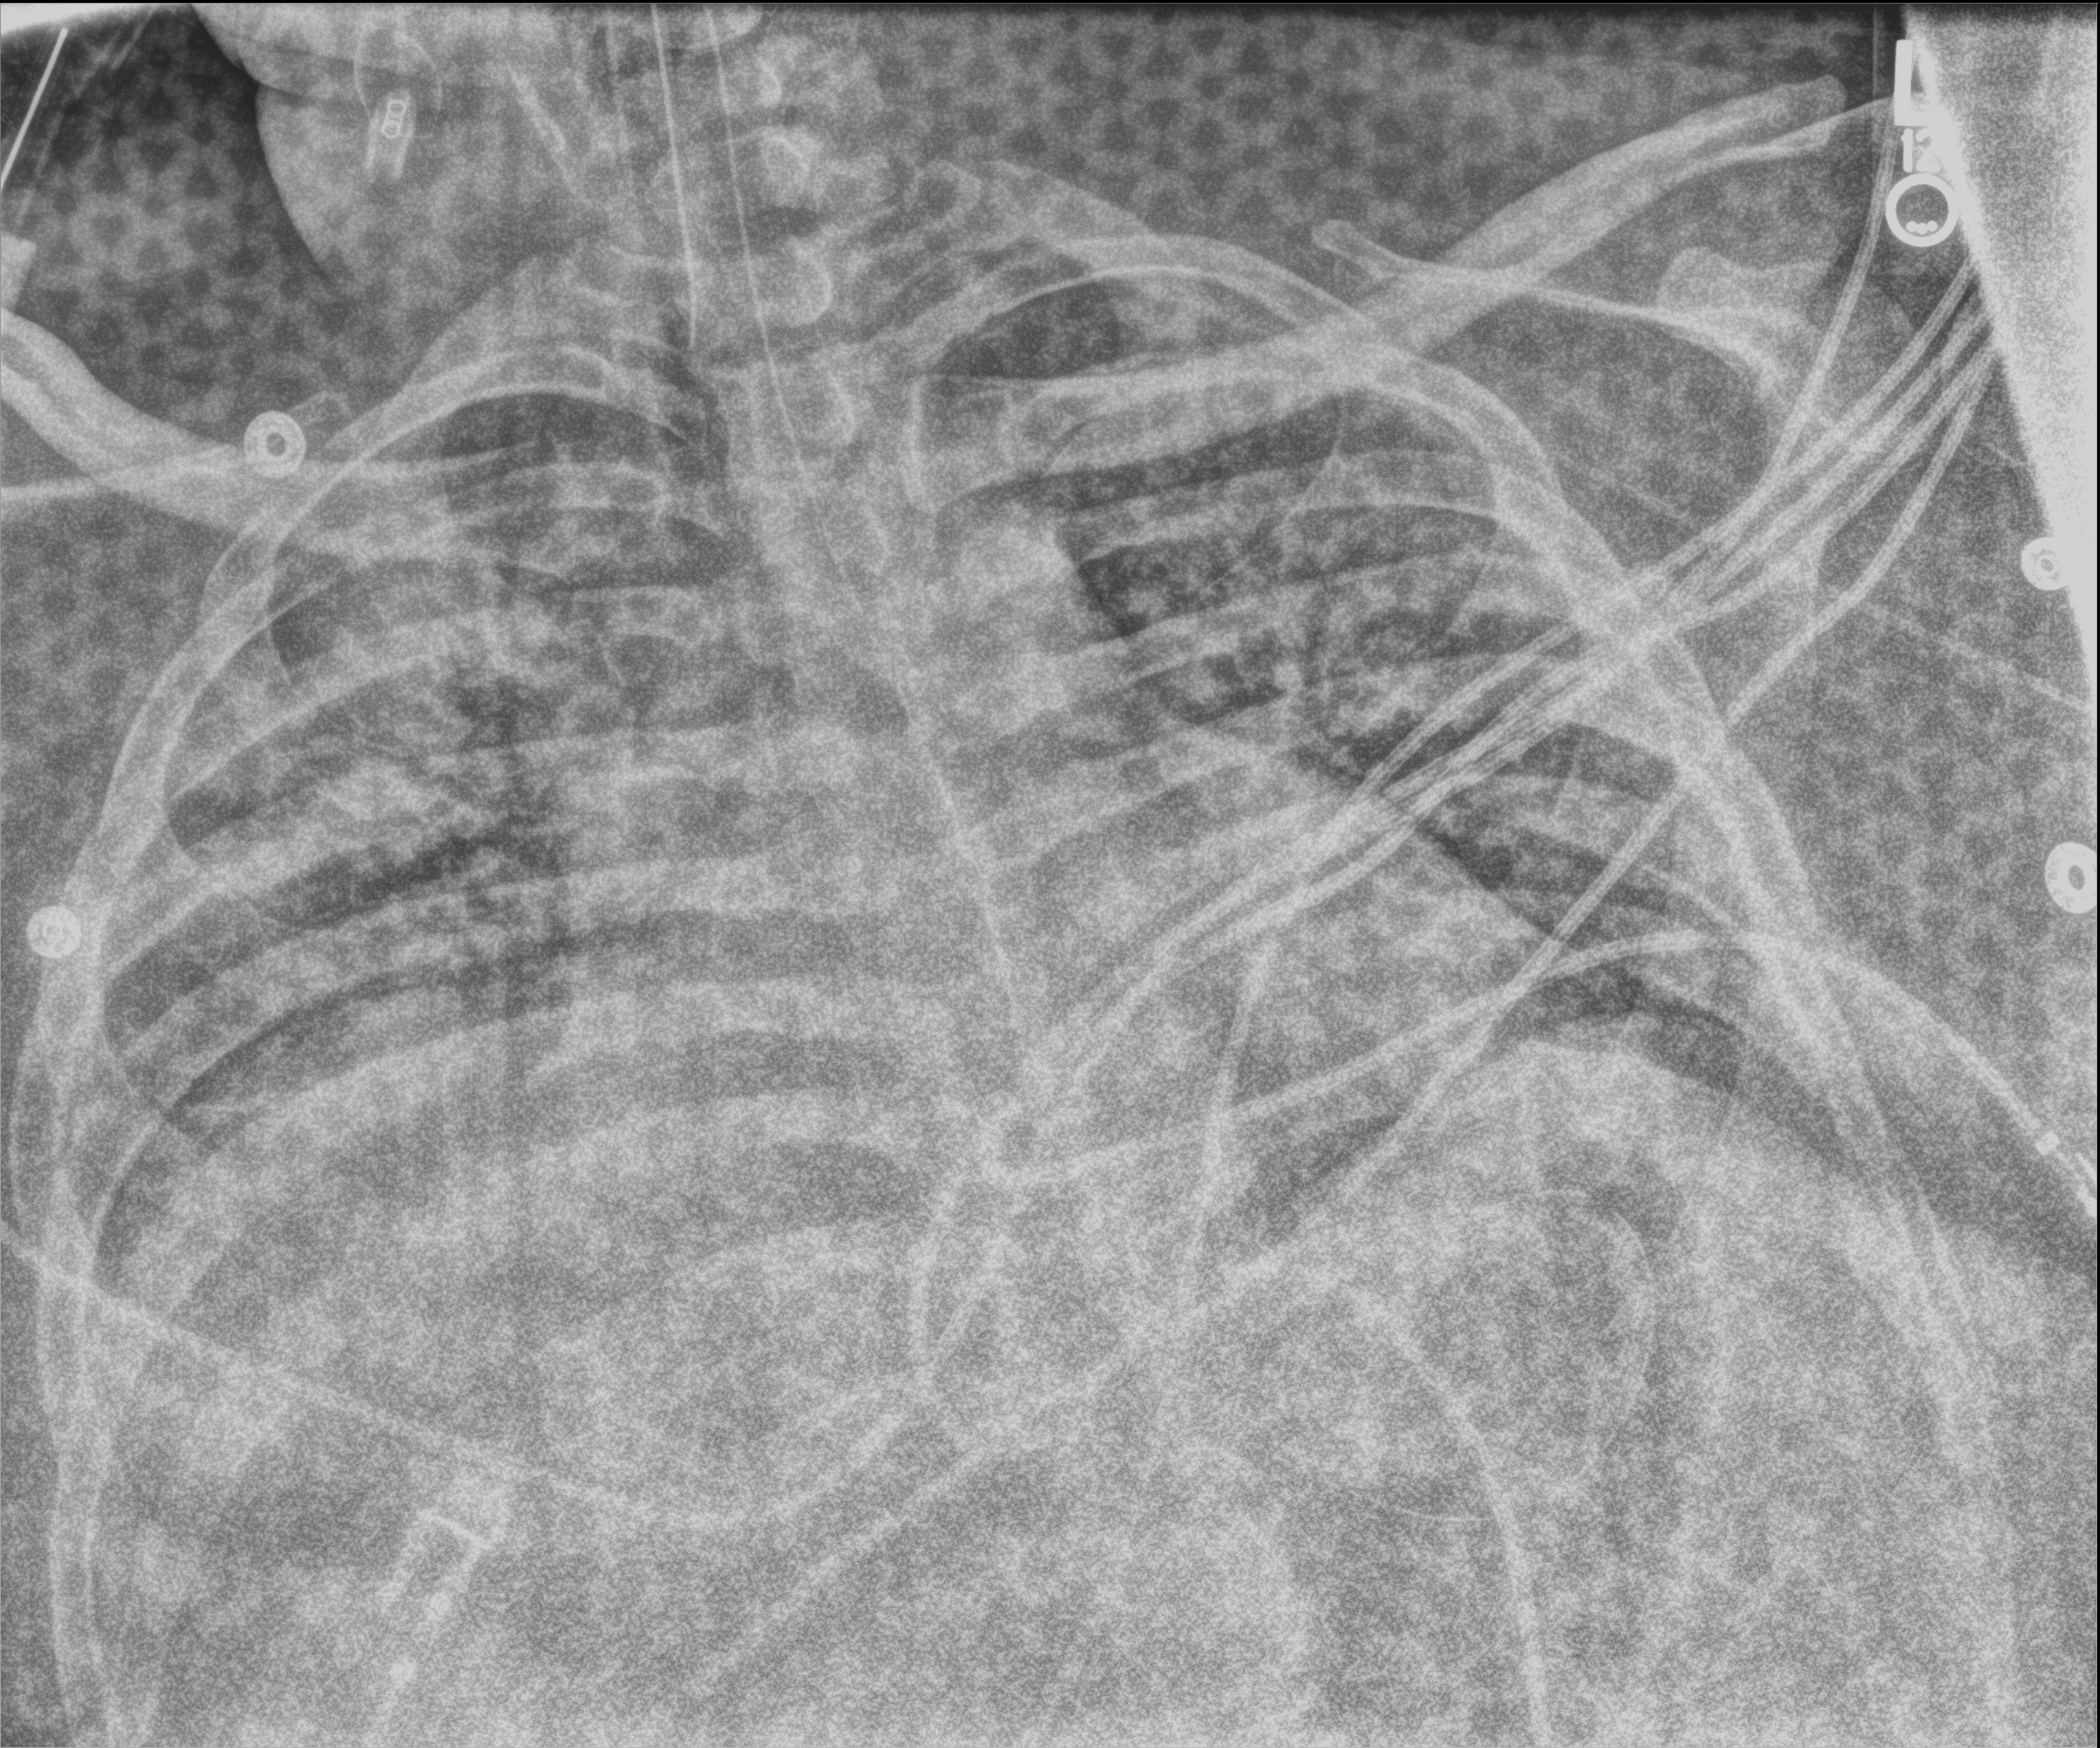
Portable chest radiograph, anteroposterior (AP) projection. Male patient hospitalised with COVID-19, age 18–59 years.
Admission-level facts for this patient (not findings on this image; timing relative to this image not recorded):
- admitted to intensive care during this hospital stay: yes
- COPD (admission record): yes